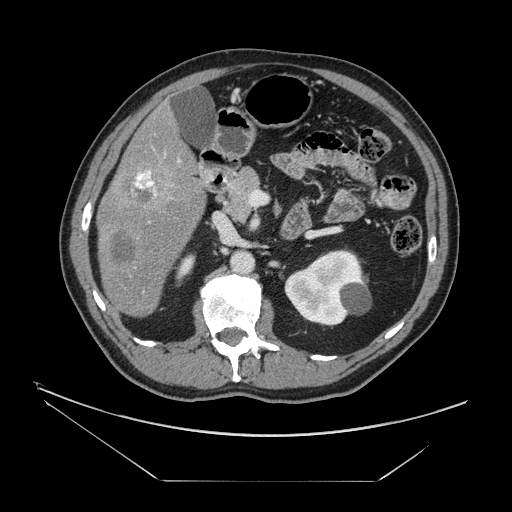
Contrast-enhanced abdominal CT, one axial slice. Slice 71 of 161 in the series (ordered by position). 120 kVp. Intravenous contrast given. Soft-tissue window (W 400 / L 40 HU). 2.5 mm slice thickness. 512 × 512 image matrix. Male patient, age 65 years. Case-level facts recorded for this patient, not image findings: diagnosis: colorectal cancer liver metastases, imaged before liver resection.
Structures marked on this image (outlined manually by an expert reader):
- liver: bounding box (x1, y1, x2, y2) in pixels: (99, 107, 206, 316)
- portal vein (with intrahepatic branches): (135, 160, 180, 195)
- liver metastasis: (113, 236, 139, 266)
- liver metastasis: (124, 170, 159, 205)